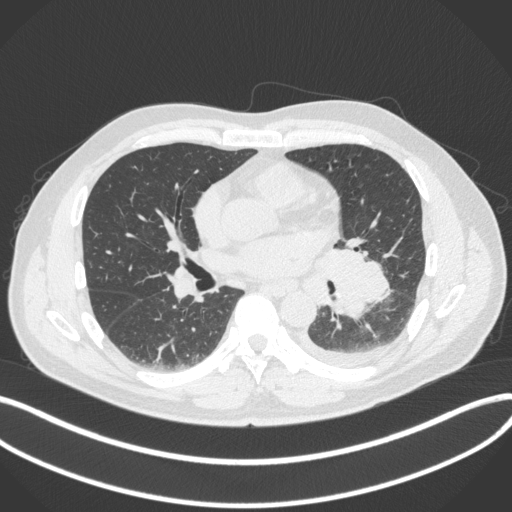
Chest CT, one axial slice. Position 181 of 350 along the scan axis. Lung window (W 1500 / L -600 HU). 1 mm slice thickness. 512 × 512 image matrix, field of view 400 × 400 mm. Male patient, age 58 years. From the clinical record (not read from this slice): clinical TNM (as recorded): T3 N1 M1b.
Outlined on this slice (bounding box drawn by a radiologist):
- lung tumour (recorded histology: small cell carcinoma): box from (x=321, y=239) to (x=393, y=314) px